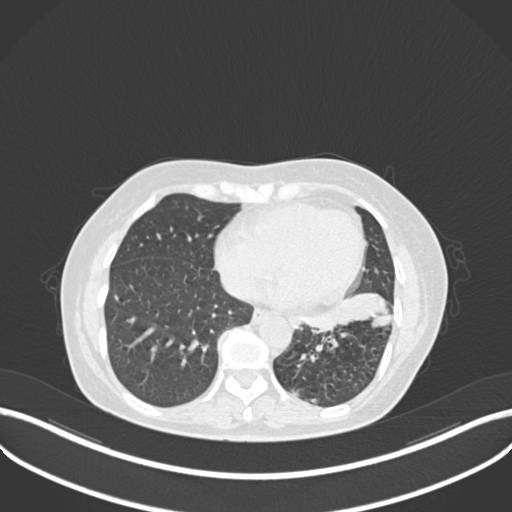
Chest CT, one axial slice; position 92 of 270 along the scan axis; reconstruction kernel B30f; lung window (W 1500 / L -600 HU); 512 × 512 image matrix, field of view 400 × 400 mm. Female patient, age 63 years. Case-level facts recorded for this patient, not image findings: clinical TNM (as recorded): T1b N0 M0; histopathological grade: G2-3.
Structures marked on this image (rectangle marked by the reading radiologist):
- lung tumour (recorded histology: adenocarcinoma): bounding box (x1, y1, x2, y2) in pixels: (289, 285, 392, 334)